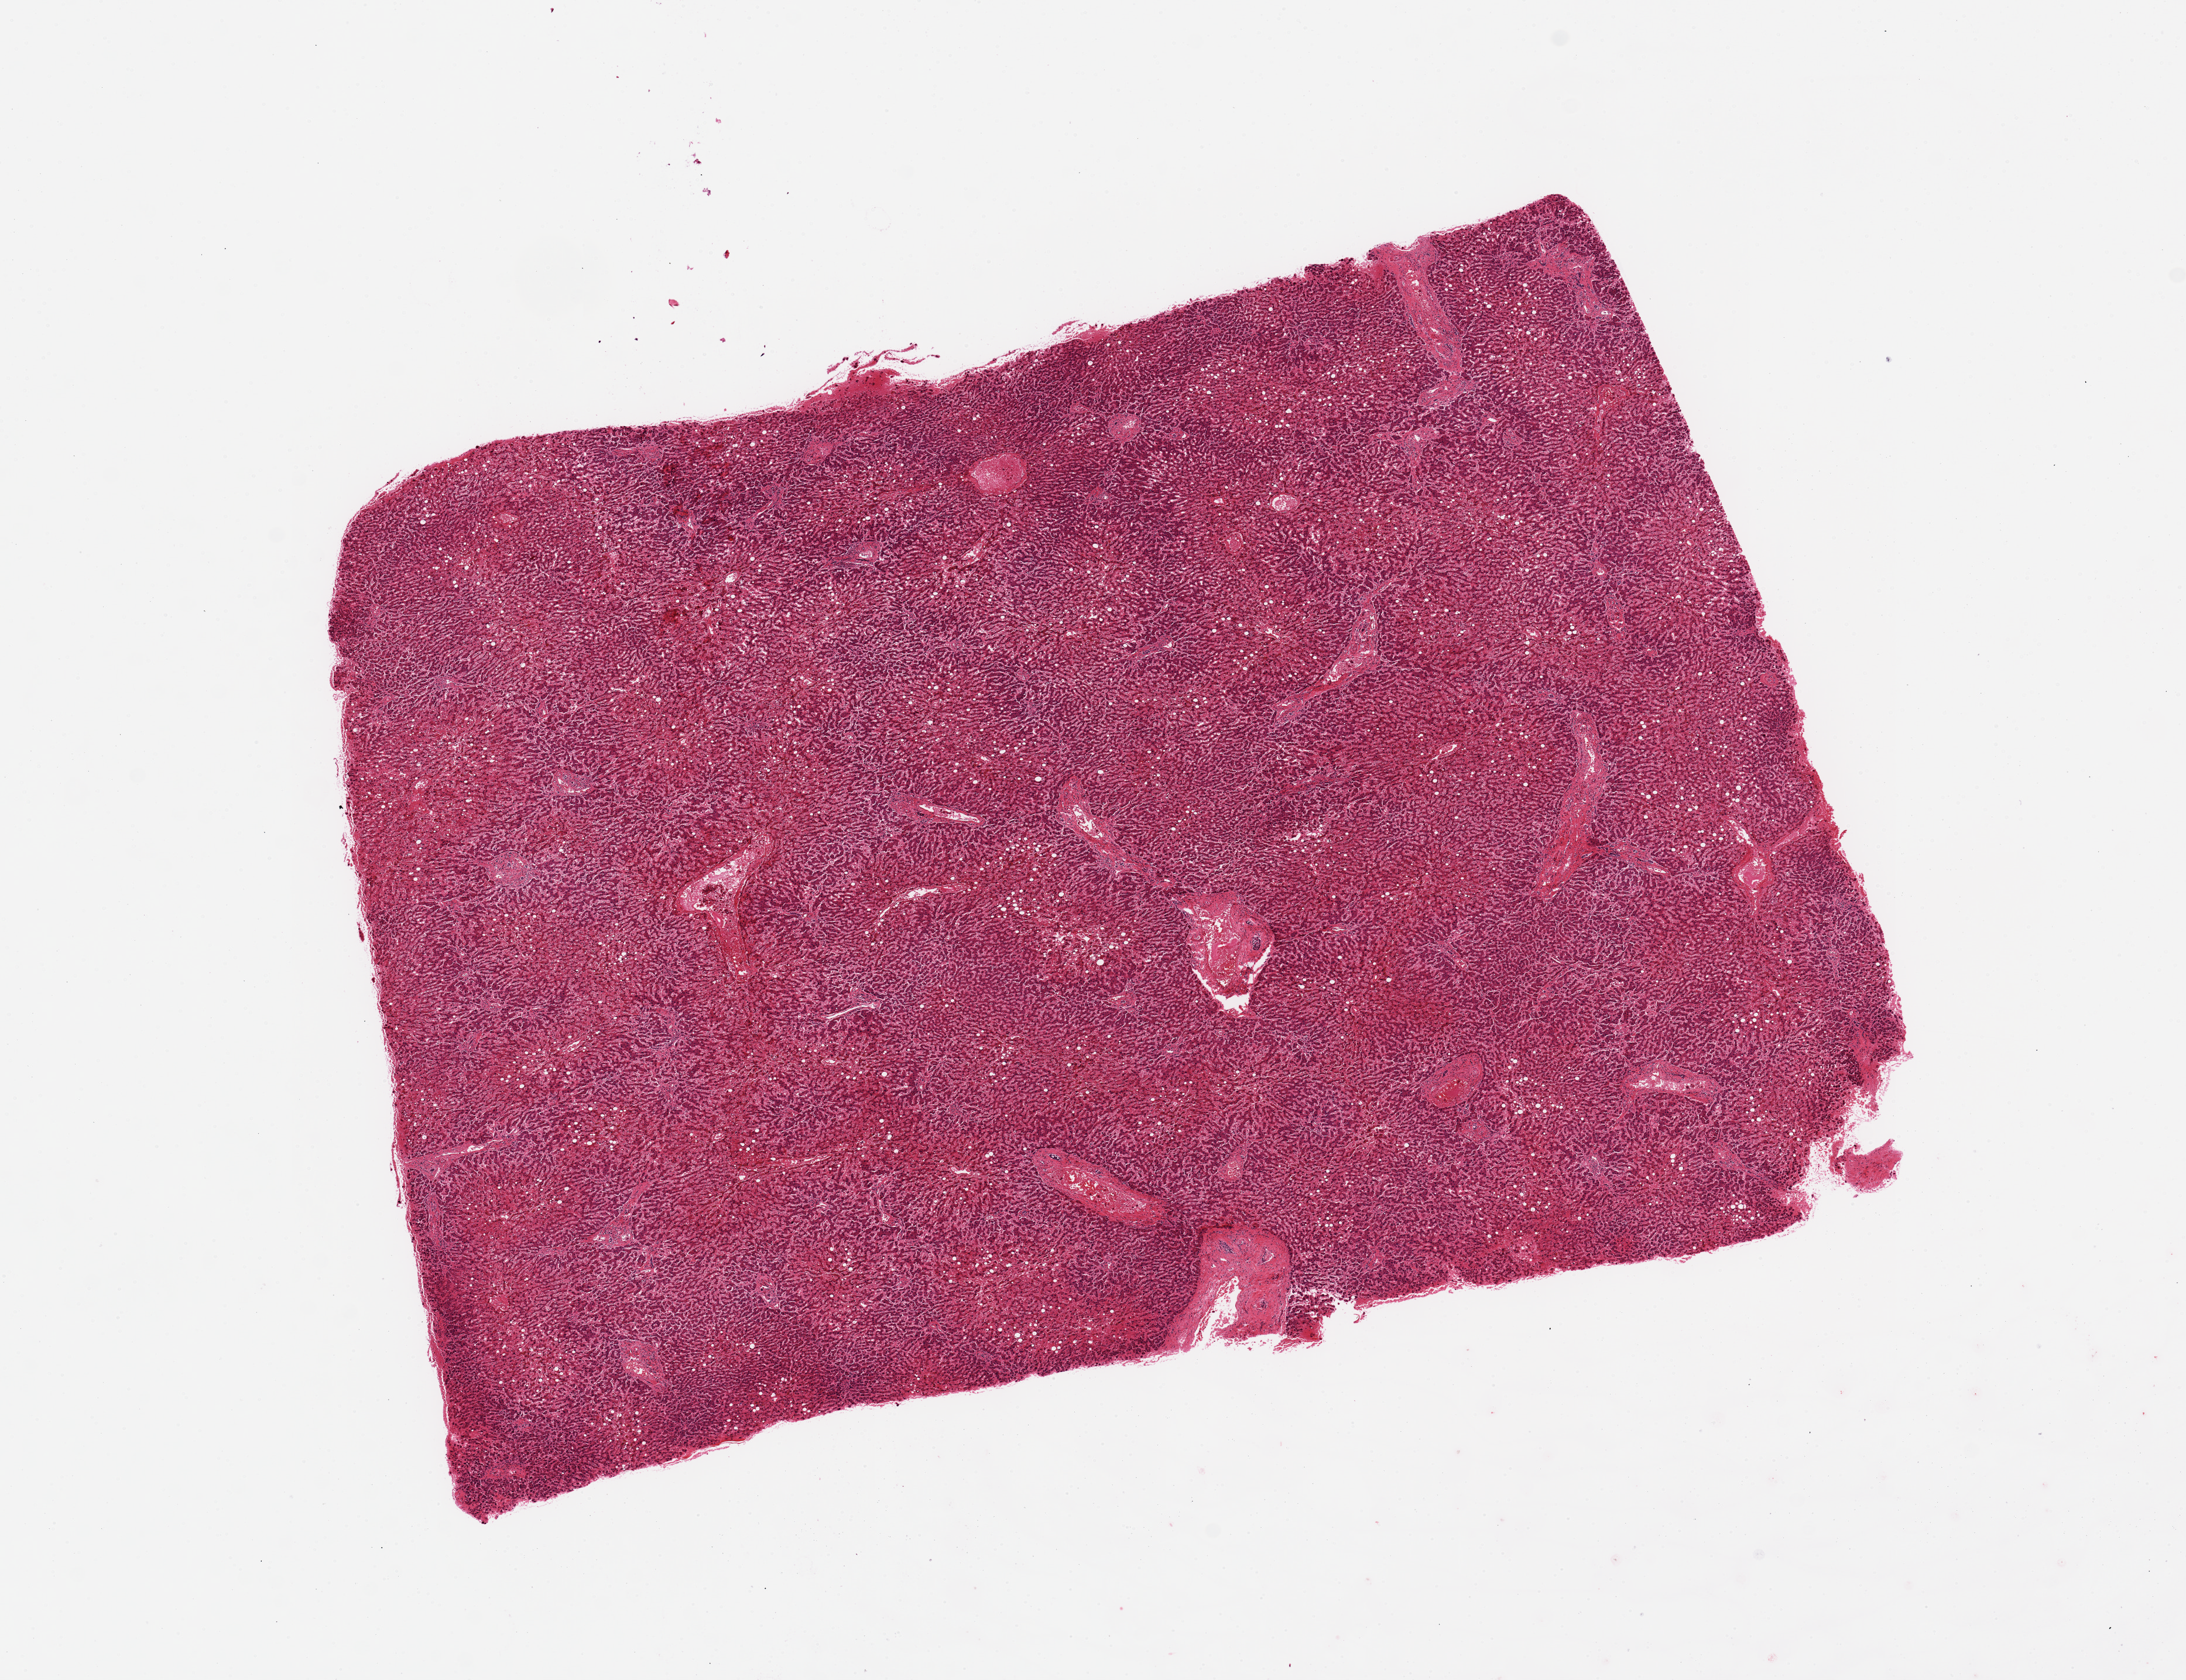
Digitized hematoxylin and eosin (H&E)-stained section, a low-resolution overview of the entire scanned area, about 14.8 x 11.3 mm (slide scanned at 20x), PAXgene-fixed paraffin-embedded (PFPE) section, target tissue: liver, donor tissue sample. Male donor.
- review note (as recorded): Mild congestion